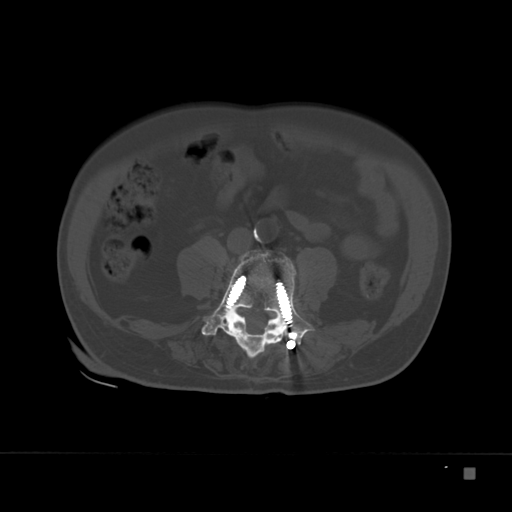
CT including the spine, one axial slice; slice 46 of 332 in the series (ordered by position); bone window (W 1800 / L 400 HU); 1.5 mm slice thickness; 512 × 512 image matrix, field of view 389 × 389 mm. Male patient, age 72 years. From the clinical record (not read from this slice): primary cancer: skeletal.
Outlined on this slice (semi-automatic segmentation, software-assisted and operator-edited):
- L4 vertebra: bounding box (x1, y1, x2, y2) in pixels: (202, 249, 315, 359)